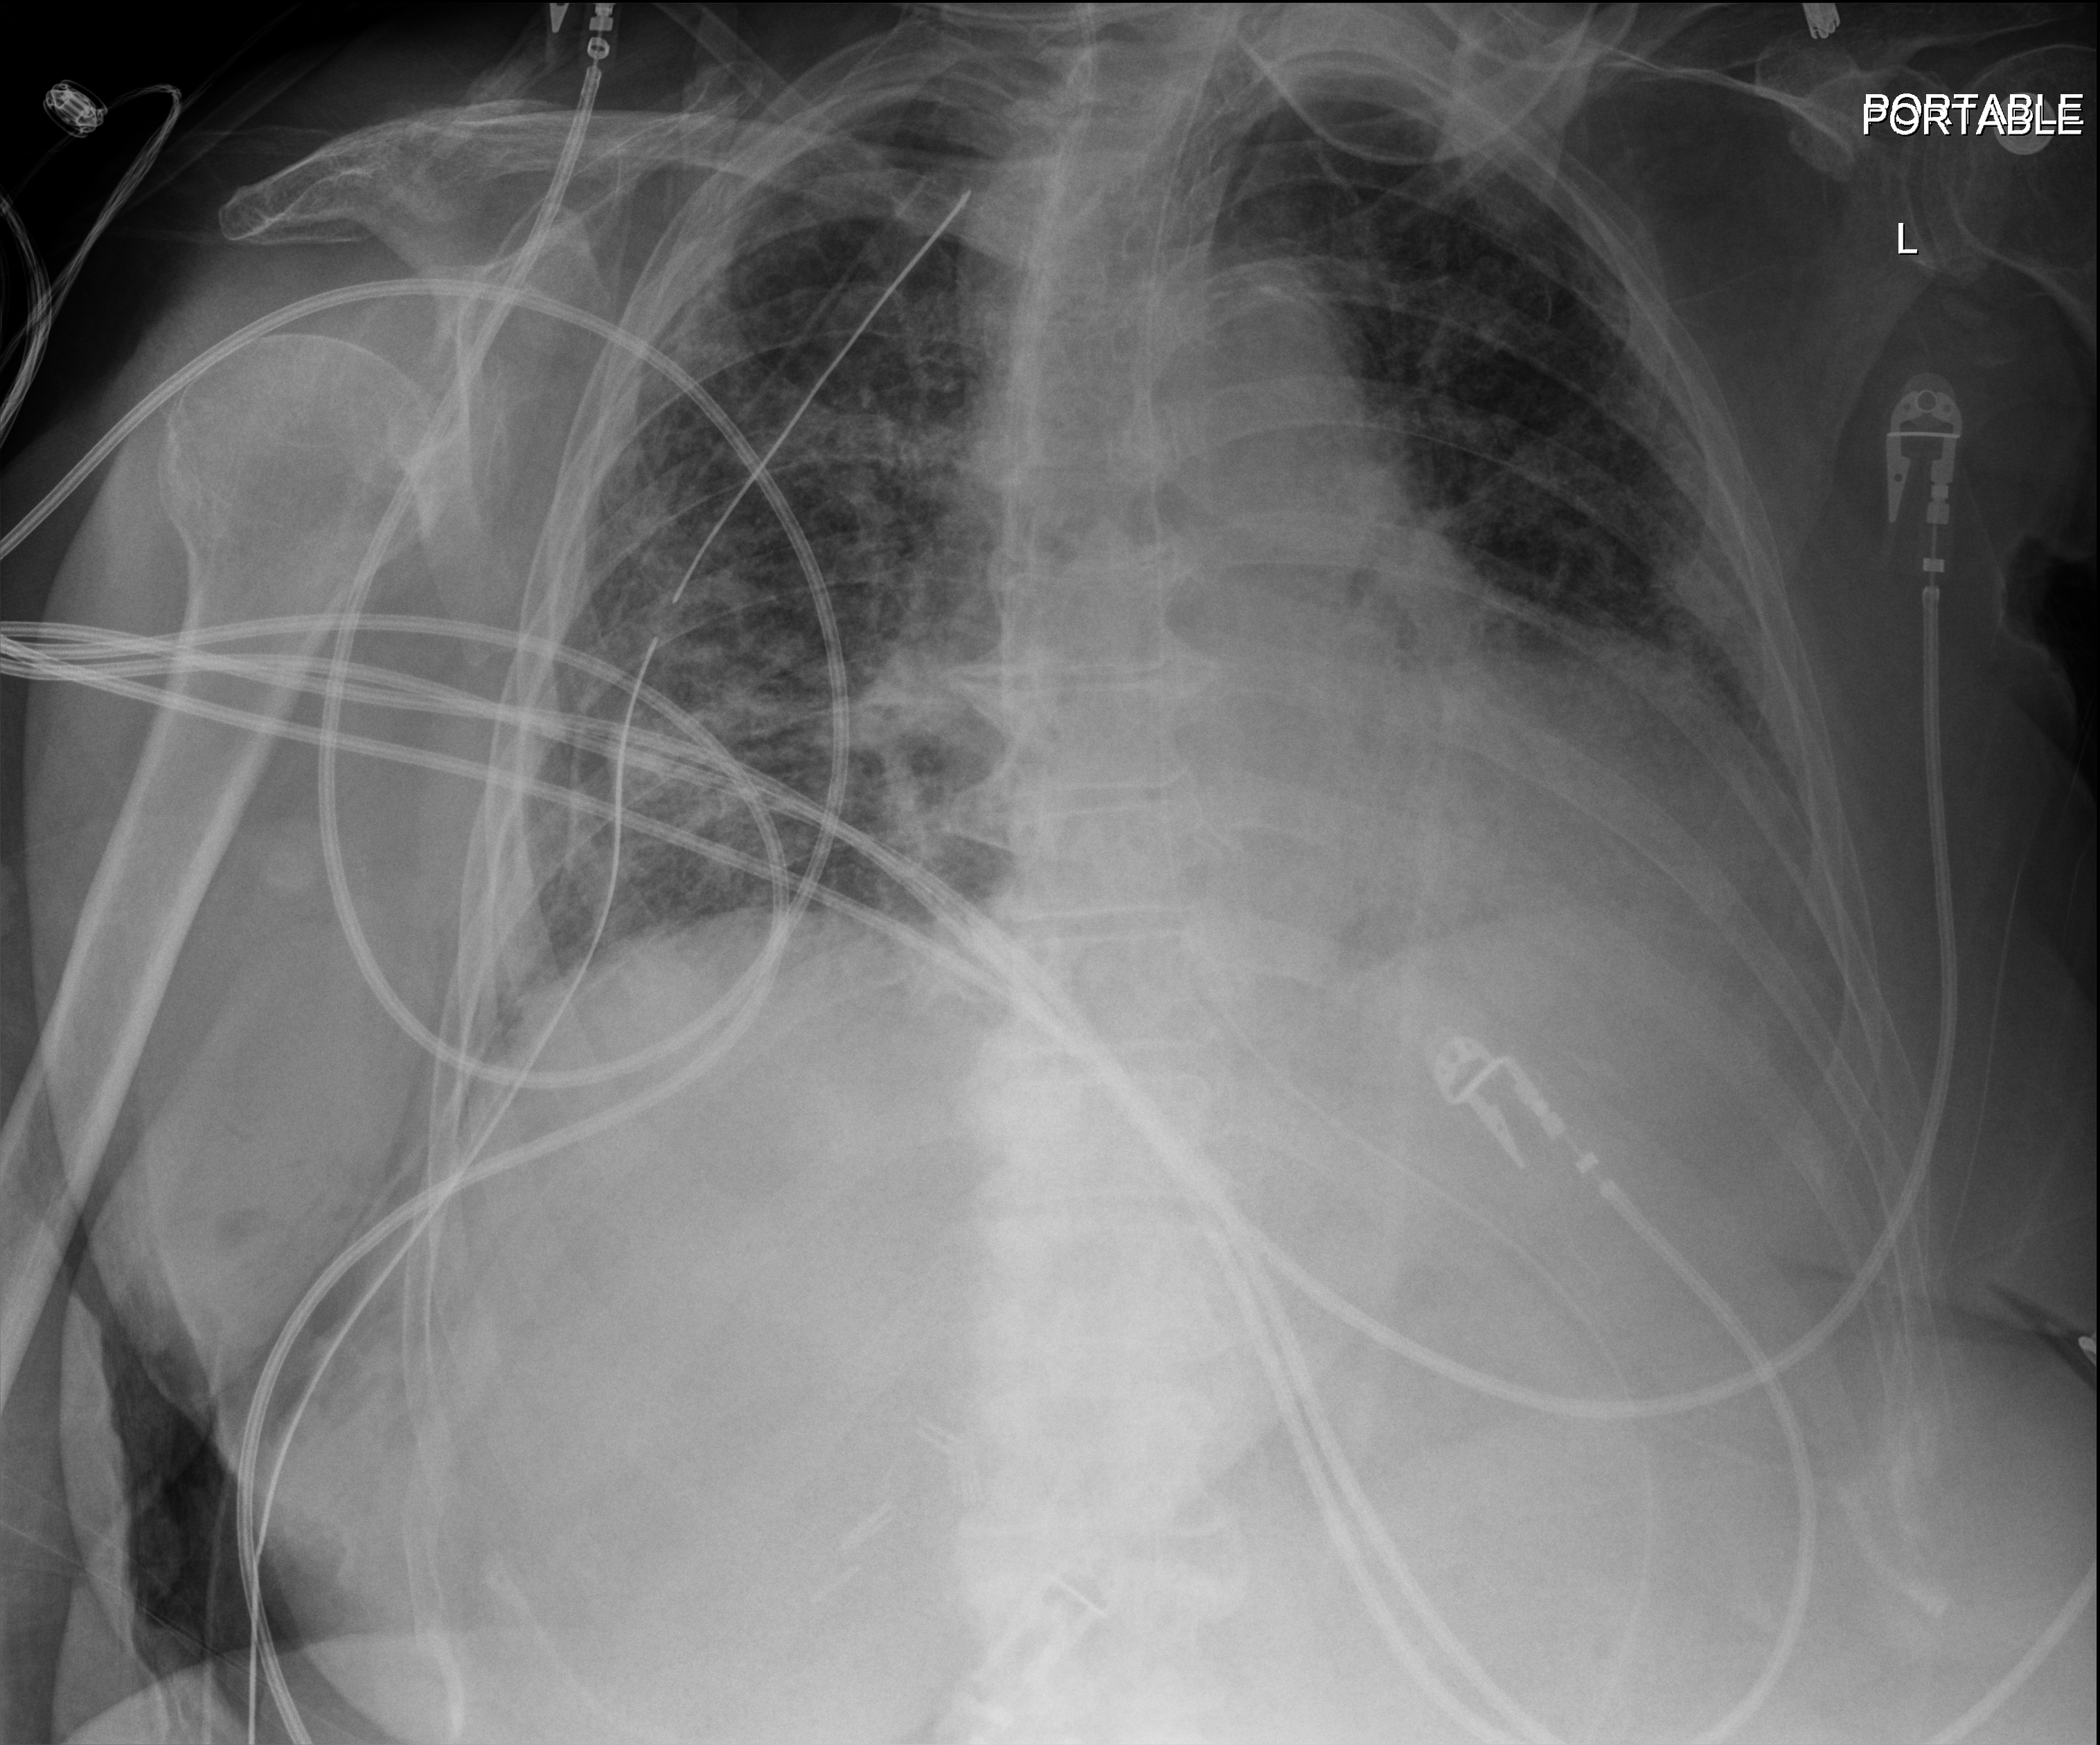
Portable chest radiograph, anteroposterior (AP) projection. Female patient hospitalised with COVID-19, age 75–90 years.
Hospital-stay facts (about this admission, not read from this image; timing relative to this image not recorded): mechanically ventilated during this hospital stay: yes.